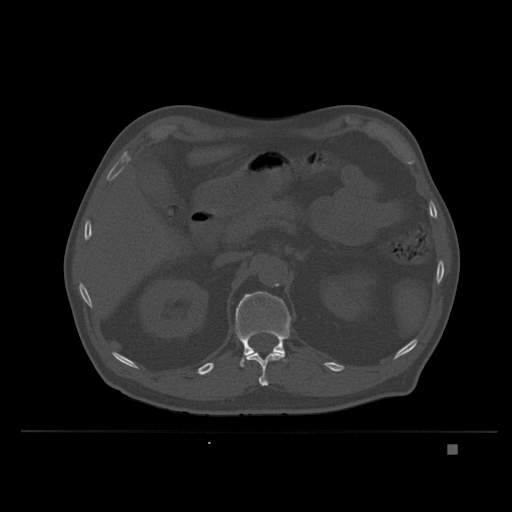
CT including the spine, one axial slice. Position 147 of 435 along the scan axis. Bone window (W 1800 / L 400 HU). 1.5 mm slice thickness. 512 × 512 image matrix, field of view 434 × 434 mm. Male patient, age 73 years. From the clinical record (not read from this slice): primary cancer: skin.
Annotated regions visible in this slice (semi-automatically segmented with operator editing):
- L1 vertebra: bounding box [x1, y1, x2, y2] px = [235, 291, 291, 367]
- T12 vertebra: [246, 351, 285, 386]